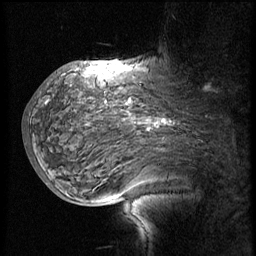
Breast MRI (dynamic contrast-enhanced), one sagittal slice; position 39 of 60 along the scan axis; 3 images stored at this slice position (order not interpretable as contrast timing); 1.5 T; TE 4.2 ms, TR 8.9 ms; 2.5 mm slice thickness; 256 × 256 image matrix, field of view 200 × 200 mm. Patient: female, 57 years. From the clinical record (not read from this slice): setting: breast cancer imaged before/during neoadjuvant chemotherapy; receptor status: HER2-positive.
Outlined on this slice (semi-automatically segmented with operator editing):
- analysis volume of interest (the breast-tissue region the enhancement analysis was run in; not a lesion): bounding box <34,75,214,171> (left, top, right, bottom; pixels)
- tumour enhancement mask (voxels above the 140 % enhancement threshold inside the analysis volume of interest): <106,101,167,126>